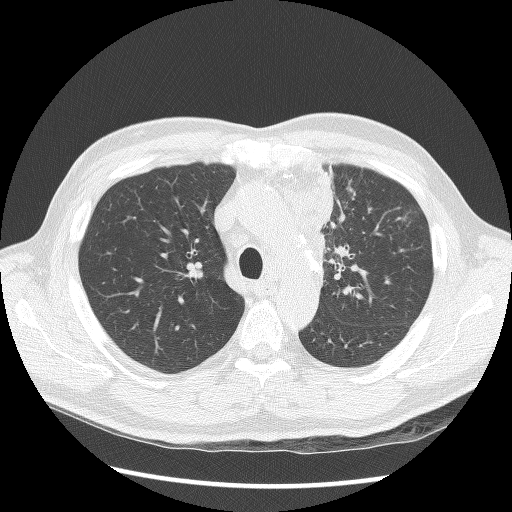
Axial slice from a low-dose chest CT screening exam. Second screening round (one year after baseline). Lung window (W 1500 / L -600 HU). 2.5 mm slice thickness. 120 kVp. Slice 37 of 136 in the series. Male, age 64 years at enrolment. Former smoker at enrolment.
Lesion marked by an expert reader, bounding box (x1, y1, x2, y2) in pixels: (296, 172, 366, 291). No non-calcified nodule or mass ≥4 mm was recorded by the screening reader at this exam. Later outcome: lung cancer diagnosed 24 days after this screen — small cell carcinoma, NOS, left upper lobe, stage IV (AJCC 6th edition), 100 mm at pathology.